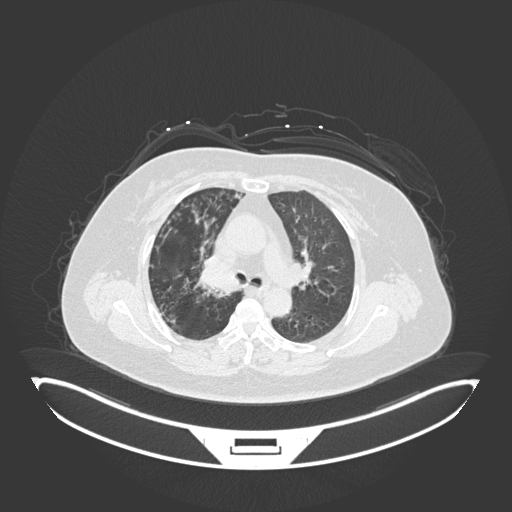
Chest CT, one axial slice. Lung window (W 1500 / L -600 HU). 512 × 512 image matrix. Patient: female, 60 years. From the clinical record (not read from this slice): clinical TNM (as recorded): T1c N0 M0; histopathological grade: G1-G2.
Structures marked on this image (rectangle marked by the reading radiologist):
- lung tumour (recorded histology: squamous cell carcinoma): bounding box <191,257,246,296> (left, top, right, bottom; pixels)